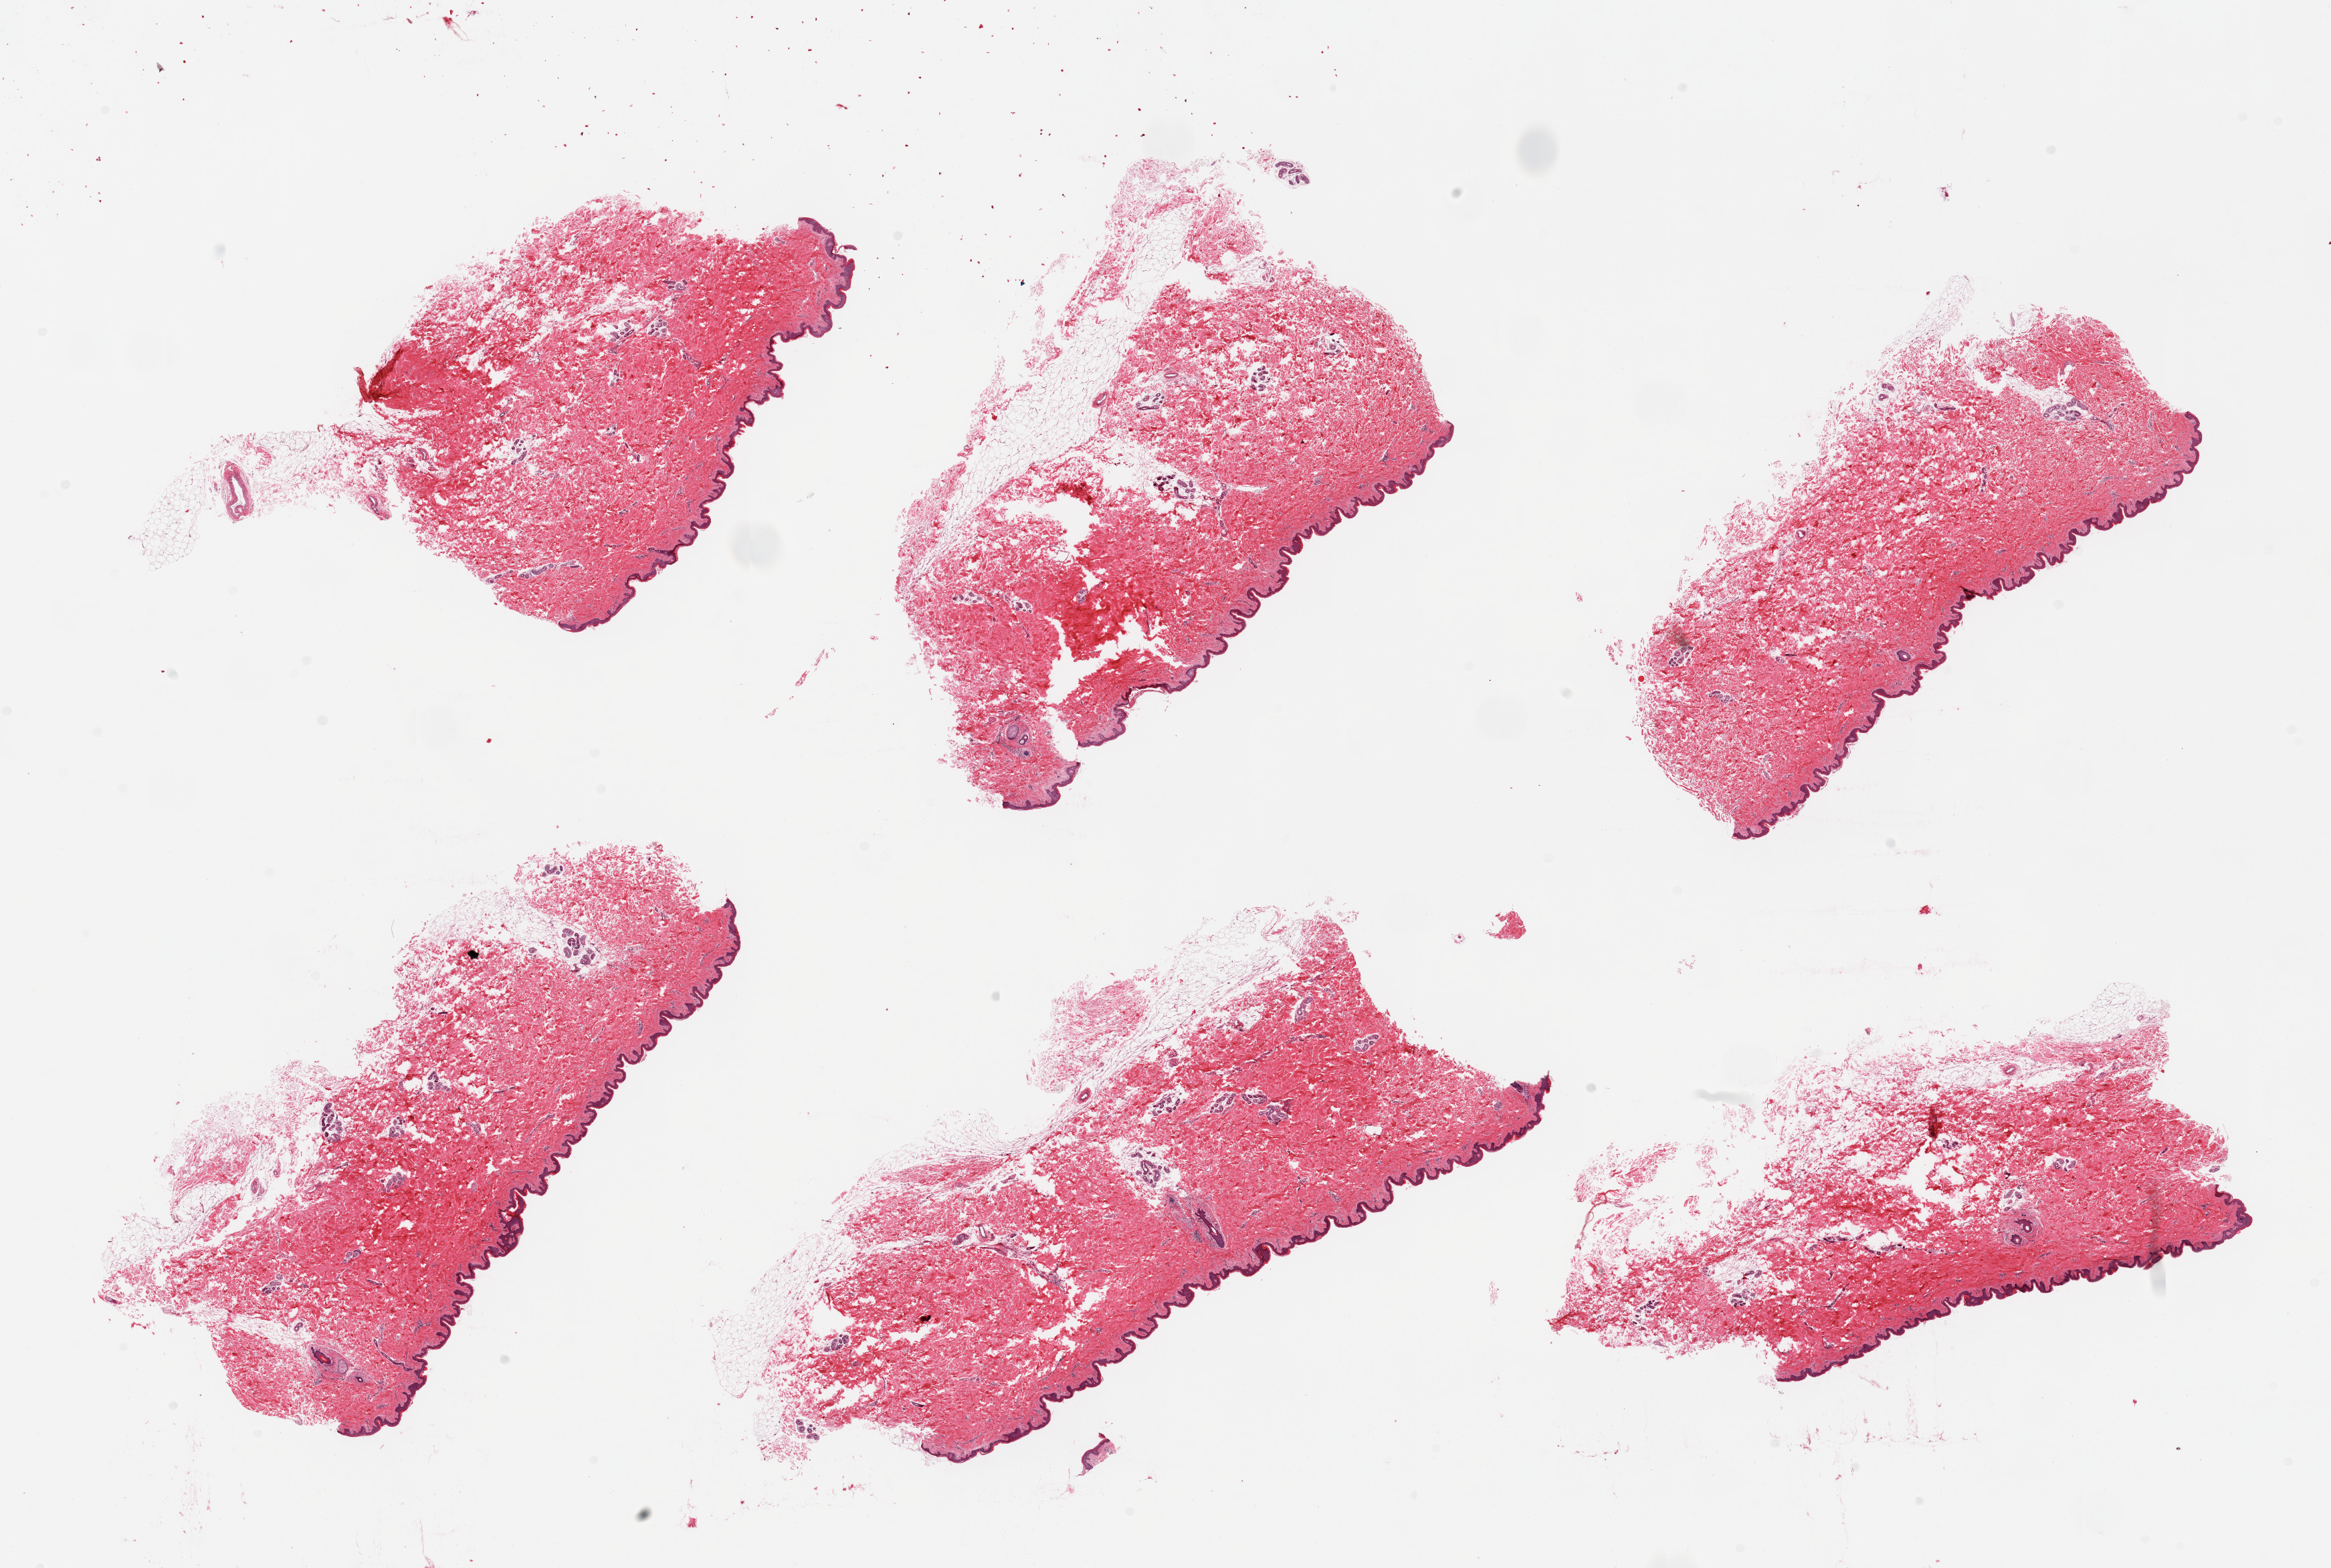
Whole-slide image, hematoxylin and eosin (H&E) stain, brightfield, low-resolution overview of the scanned area, about 27.6 x 18.5 mm, PAXgene-fixed, paraffin-embedded tissue, target tissue: skin of suprapubic region, tissue donor sample. Donor: female.
Review note (as recorded): 6 pieces; include up to 10-20% attached fat.